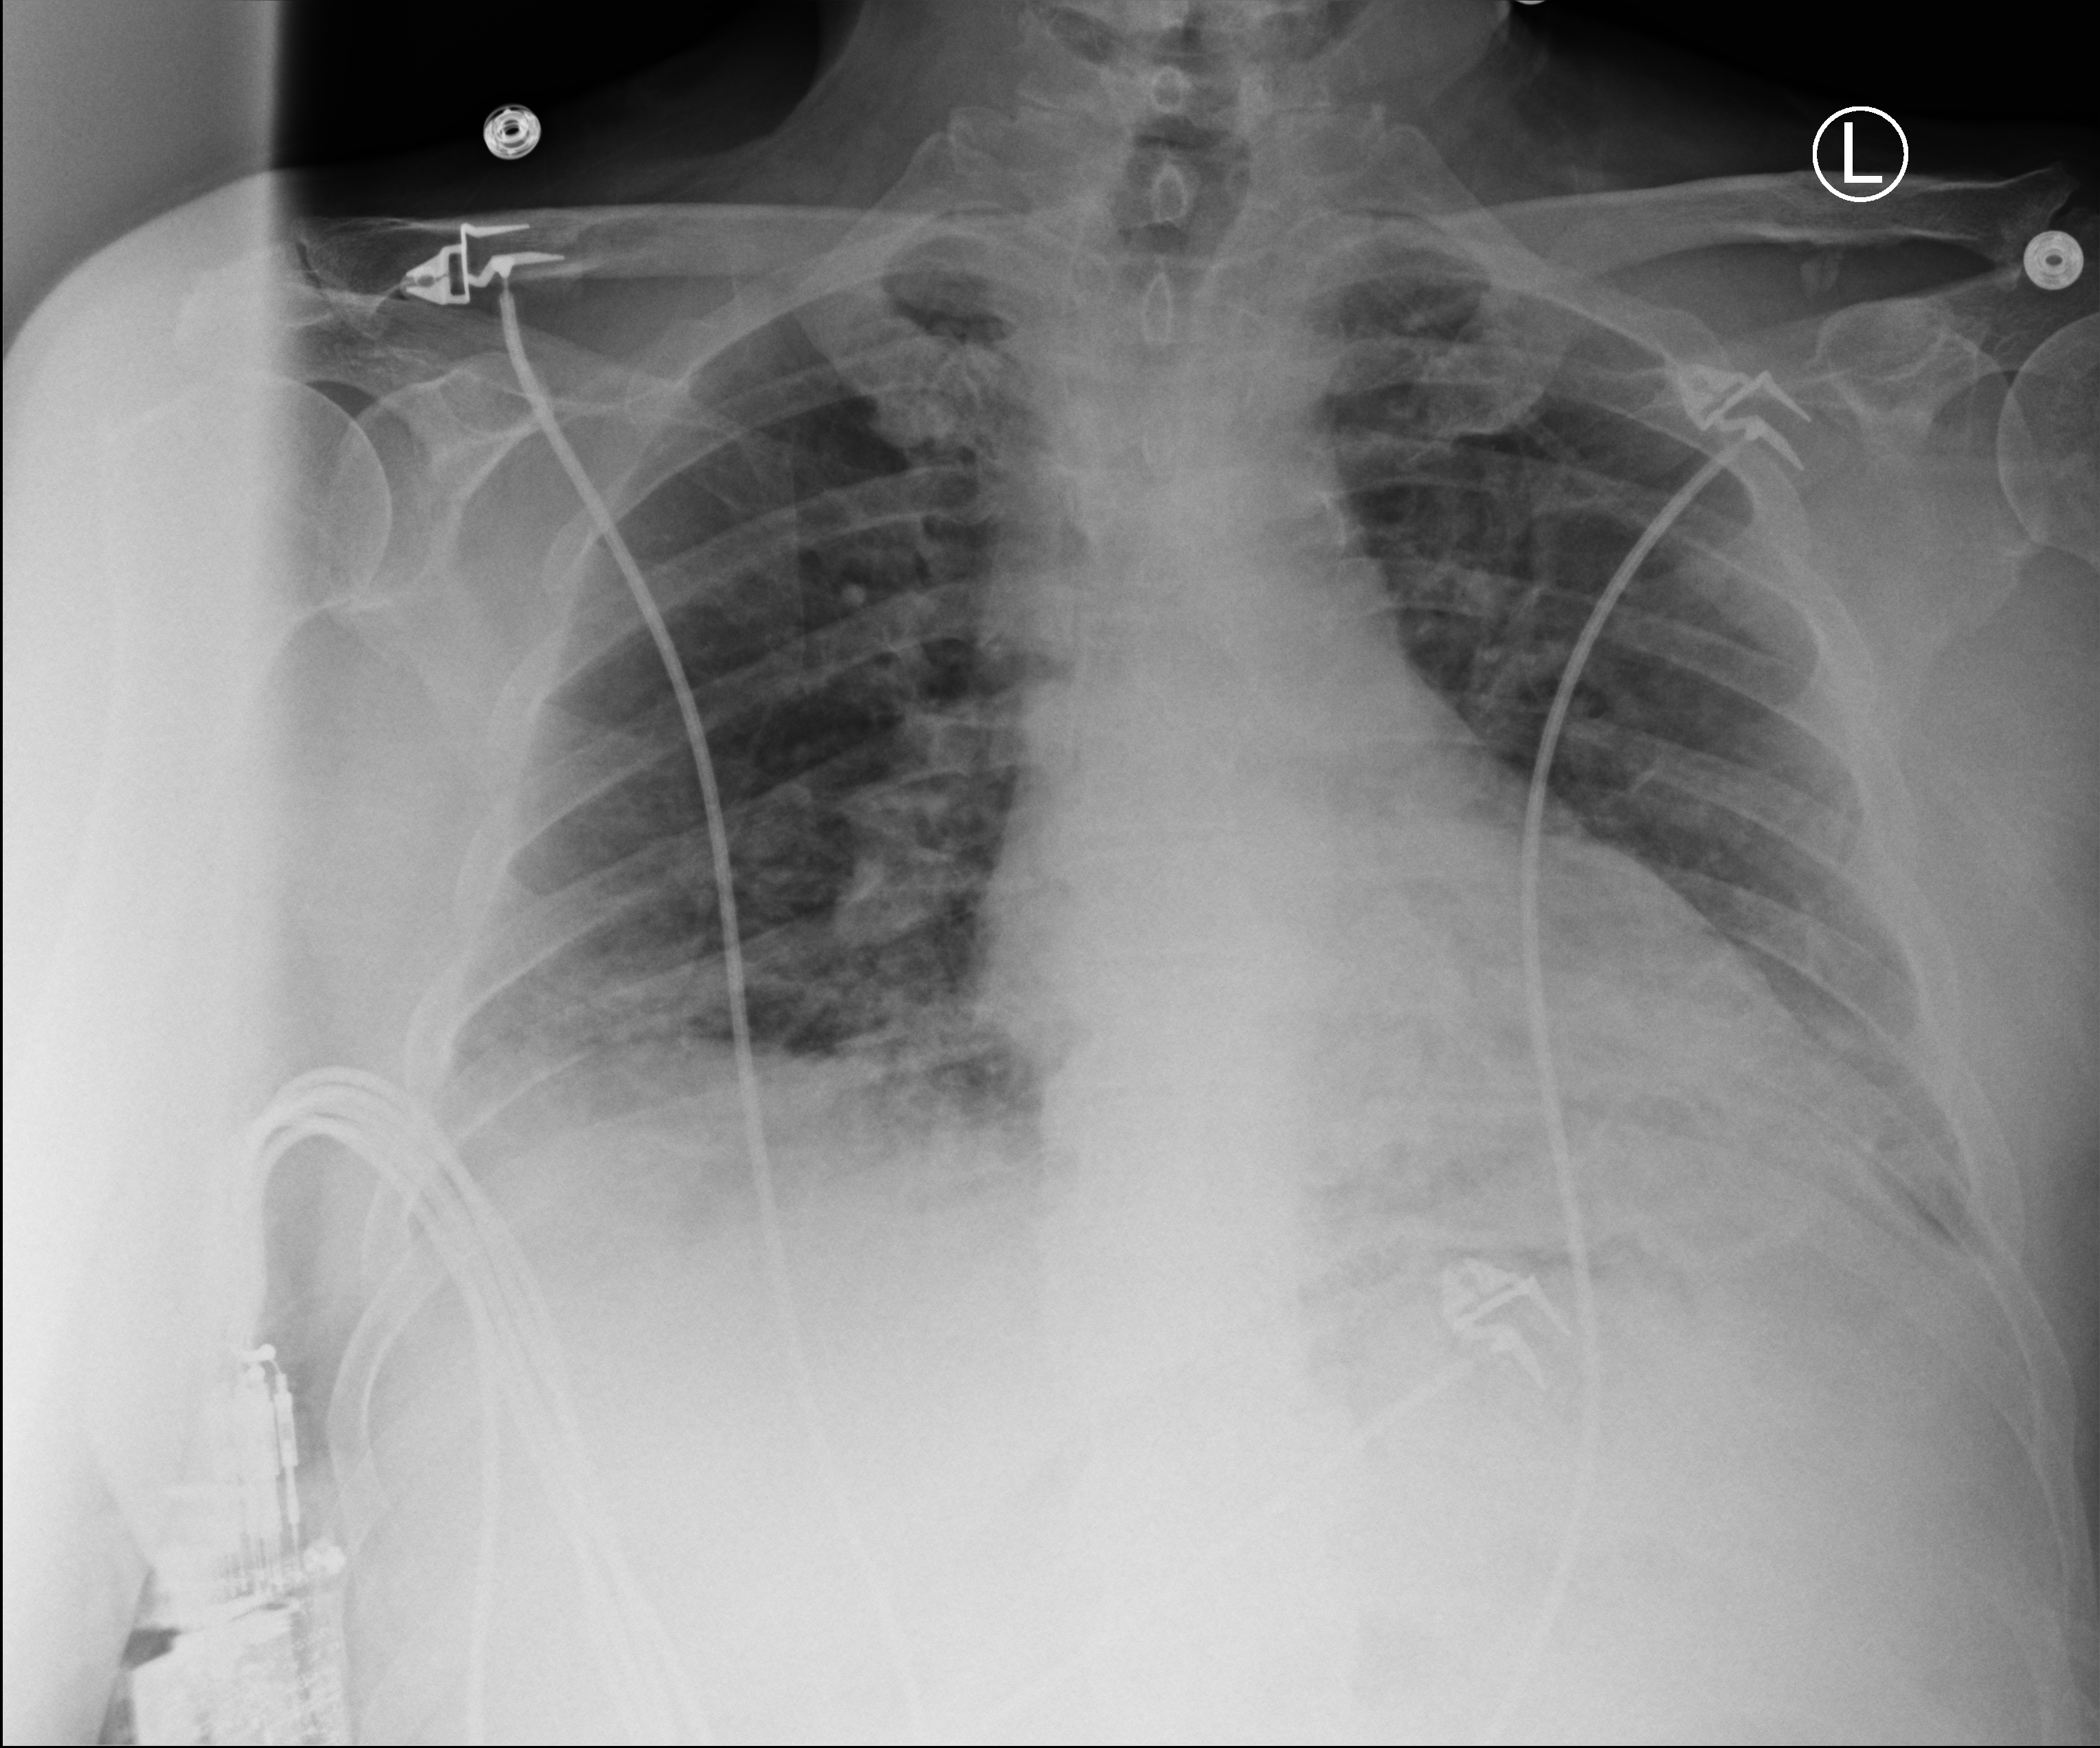
Bedside chest radiograph (computed radiography); anteroposterior (AP) projection. Patient hospitalised with COVID-19; male, aged 18–59 years.
Hospital-stay facts (about this admission, not read from this image; timing relative to this image not recorded): mechanically ventilated during this hospital stay: no.